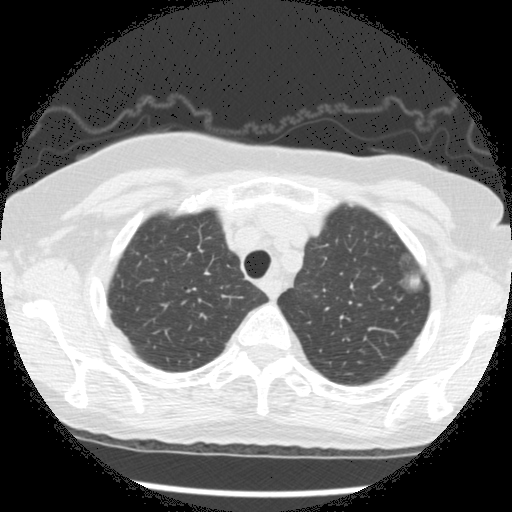
Low-dose screening chest CT, one axial slice; reconstruction kernel STANDARD; 120 kVp; lung window (W 1500 / L -600 HU); 512 × 512 image matrix, field of view 320 × 320 mm.
Structures marked on this image (manually delineated by an expert):
- lesion 1 (tumor, upper lobe of left lung): bounding box [x1, y1, x2, y2] px = [407, 274, 420, 288]